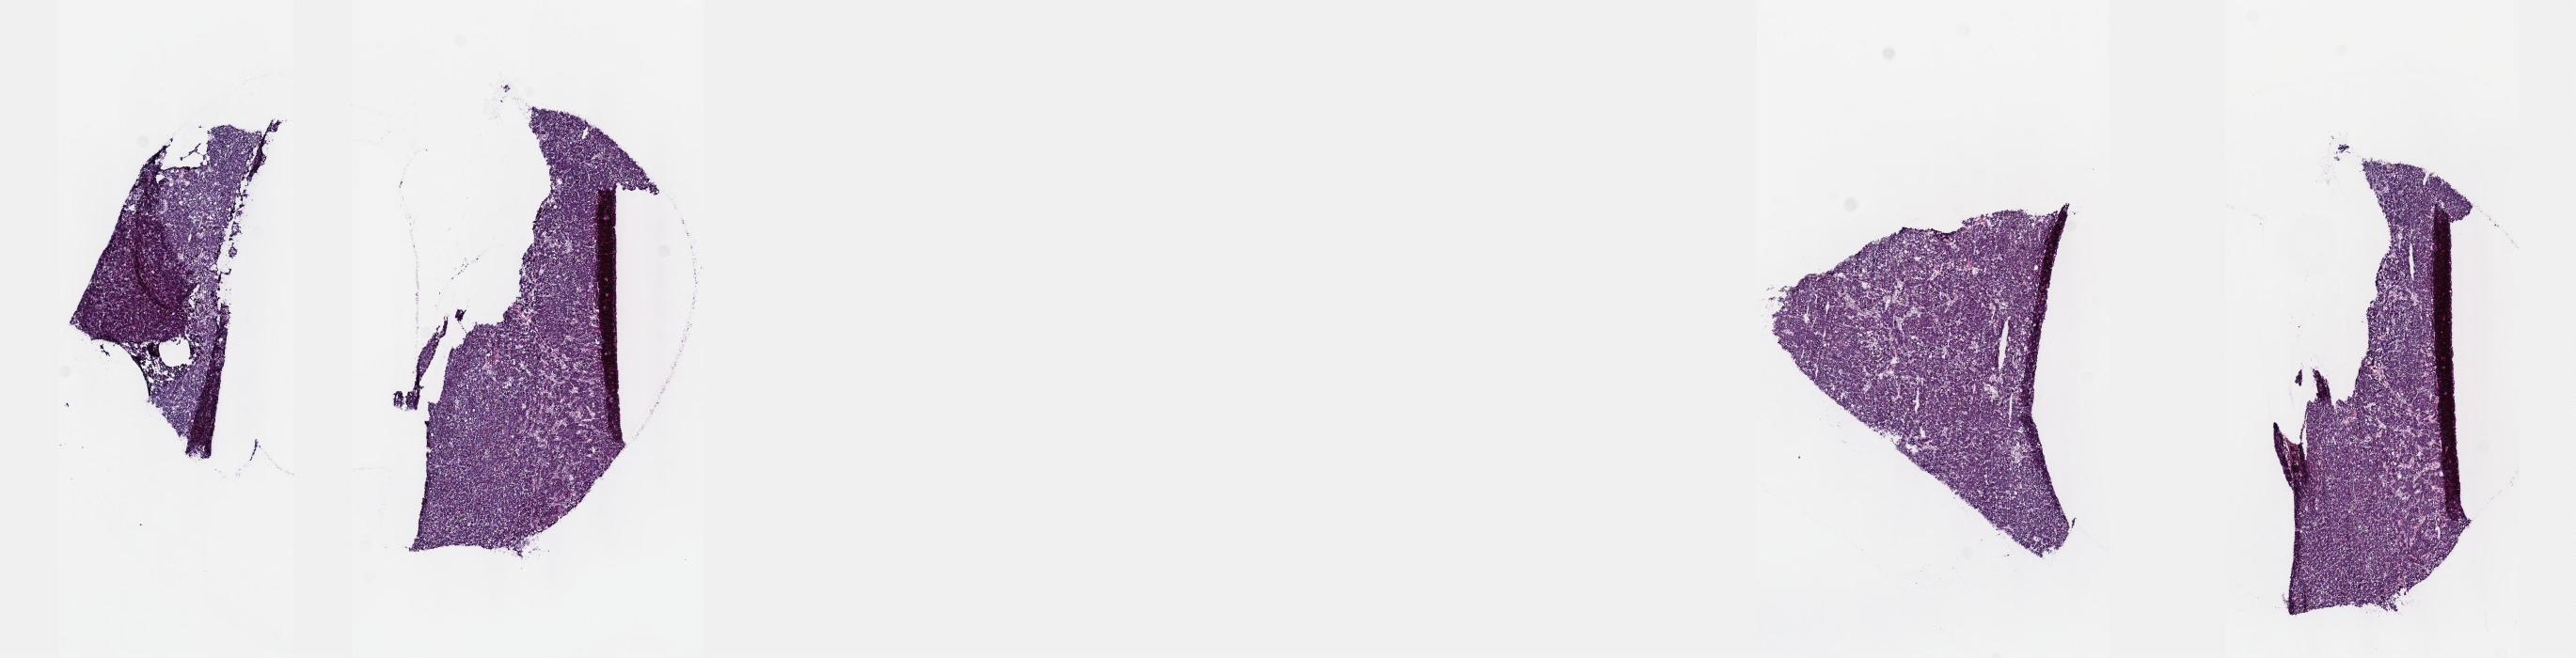
Whole-slide histology image, H&E, a low-resolution overview of the entire scanned area, about 22.1 x 5.7 mm, frozen section from the top of the tissue portion, primary tumour sample from the liver. Patient: male, age at initial diagnosis 60 years. Histologic grade: G2 (moderately differentiated). Composition of this section per pathologist review: tumour cells 100%, tumour nuclei 80%, normal cells 0%, stromal cells 0%, necrosis 0%. Inflammatory infiltration, as recorded: lymphocyte infiltration 2%, monocyte infiltration 0%, neutrophil infiltration 0%.
Diagnosis: Hepatocellular carcinoma, NOS. AJCC pathologic stage: I.